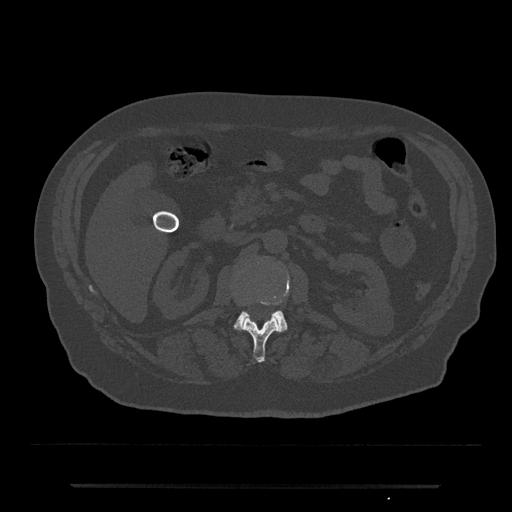
CT including the spine, one axial slice. Position 507 of 797 along the scan axis. Bone window (W 1800 / L 400 HU). 0.5 mm slice thickness. 512 × 512 image matrix, field of view 434 × 434 mm. Patient: male, 80 years. From the clinical record (not read from this slice): primary cancer: prostate; vertebrae with lytic lesions (as recorded): L1, T11.
Structures marked on this image (semi-automatically segmented with operator editing):
- L1 vertebra: box from (x=243, y=302) to (x=280, y=363) px
- L2 vertebra: (x=233, y=295)–(x=288, y=332)